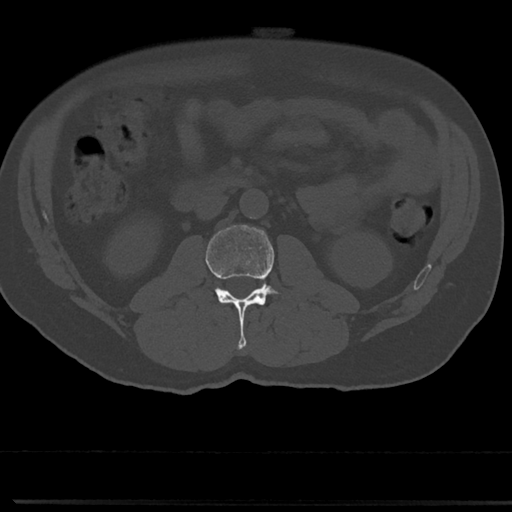
CT including the spine, one axial slice; position 7 of 817 along the scan axis; 120 kVp; bone window (W 1800 / L 400 HU); 0.5 mm slice thickness; 512 × 512 image matrix, field of view 355 × 355 mm. Male patient, age 61 years. Case-level facts recorded for this patient, not image findings: primary cancer: prostate.
Annotated regions visible in this slice (semi-automatically segmented with operator editing):
- L2 vertebra: bounding box (x1, y1, x2, y2) in pixels: (206, 225, 300, 349)